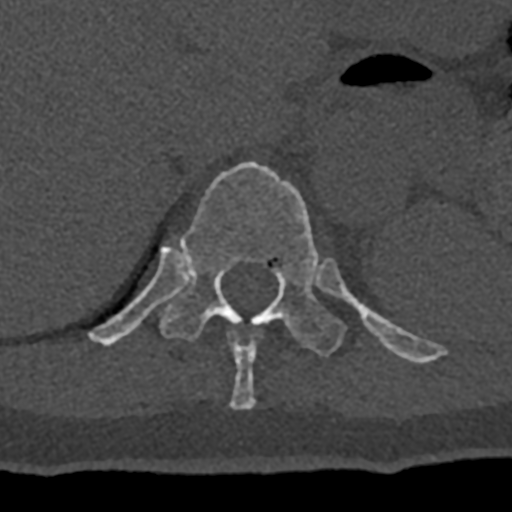
CT including the spine, one axial slice; slice 561 of 797 in the series (ordered by position); reconstruction kernel Br40s/3; 120 kVp; bone window (W 1800 / L 400 HU); 0.5 mm slice thickness; 512 × 512 image matrix, field of view 160 × 160 mm. Male patient, age 74 years. Case-level facts recorded for this patient, not image findings: primary cancer: renal.
Outlined on this slice (semi-automatic segmentation, software-assisted and operator-edited):
- T10 vertebra: box from (x=228, y=330) to (x=261, y=409) px
- T11 vertebra: (x=88, y=162)–(x=432, y=363)